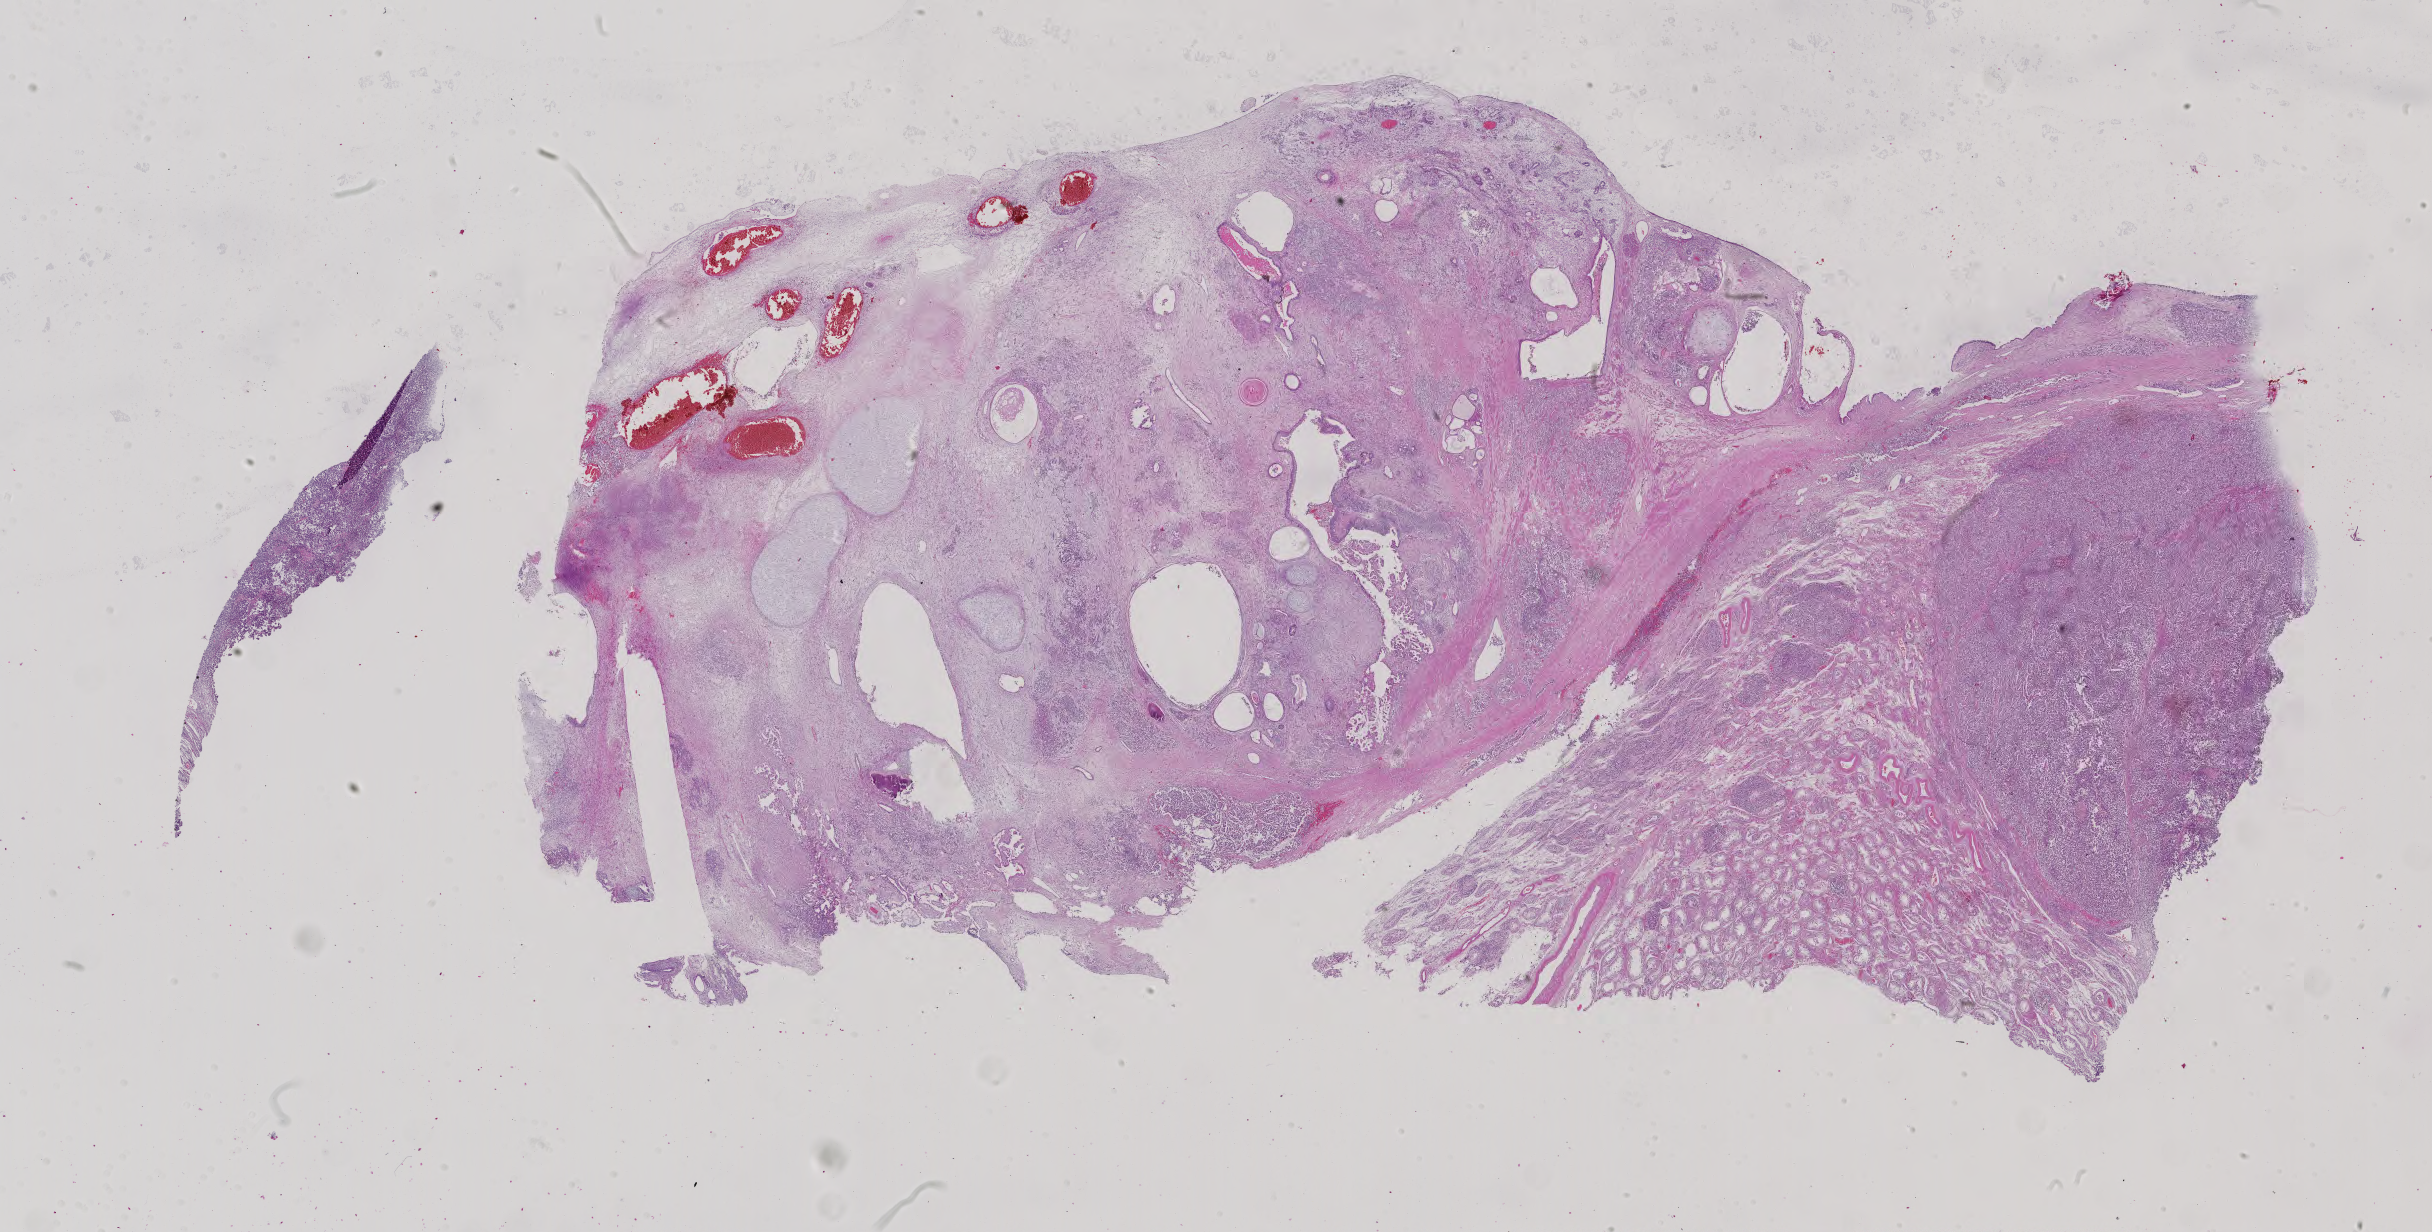
Hematoxylin and eosin (H&E) stained whole-slide image — shown as a low-resolution overview of the whole scanned area (about 35.4 x 18.0 mm). Formalin-fixed paraffin-embedded (FFPE) diagnostic section. Testis, primary tumour sample. Male, age 53 years at initial diagnosis.
* AJCC pathologic stage: IS (6th edition)
* laterality: bilateral
* pathologic diagnosis: Mixed germ cell tumor